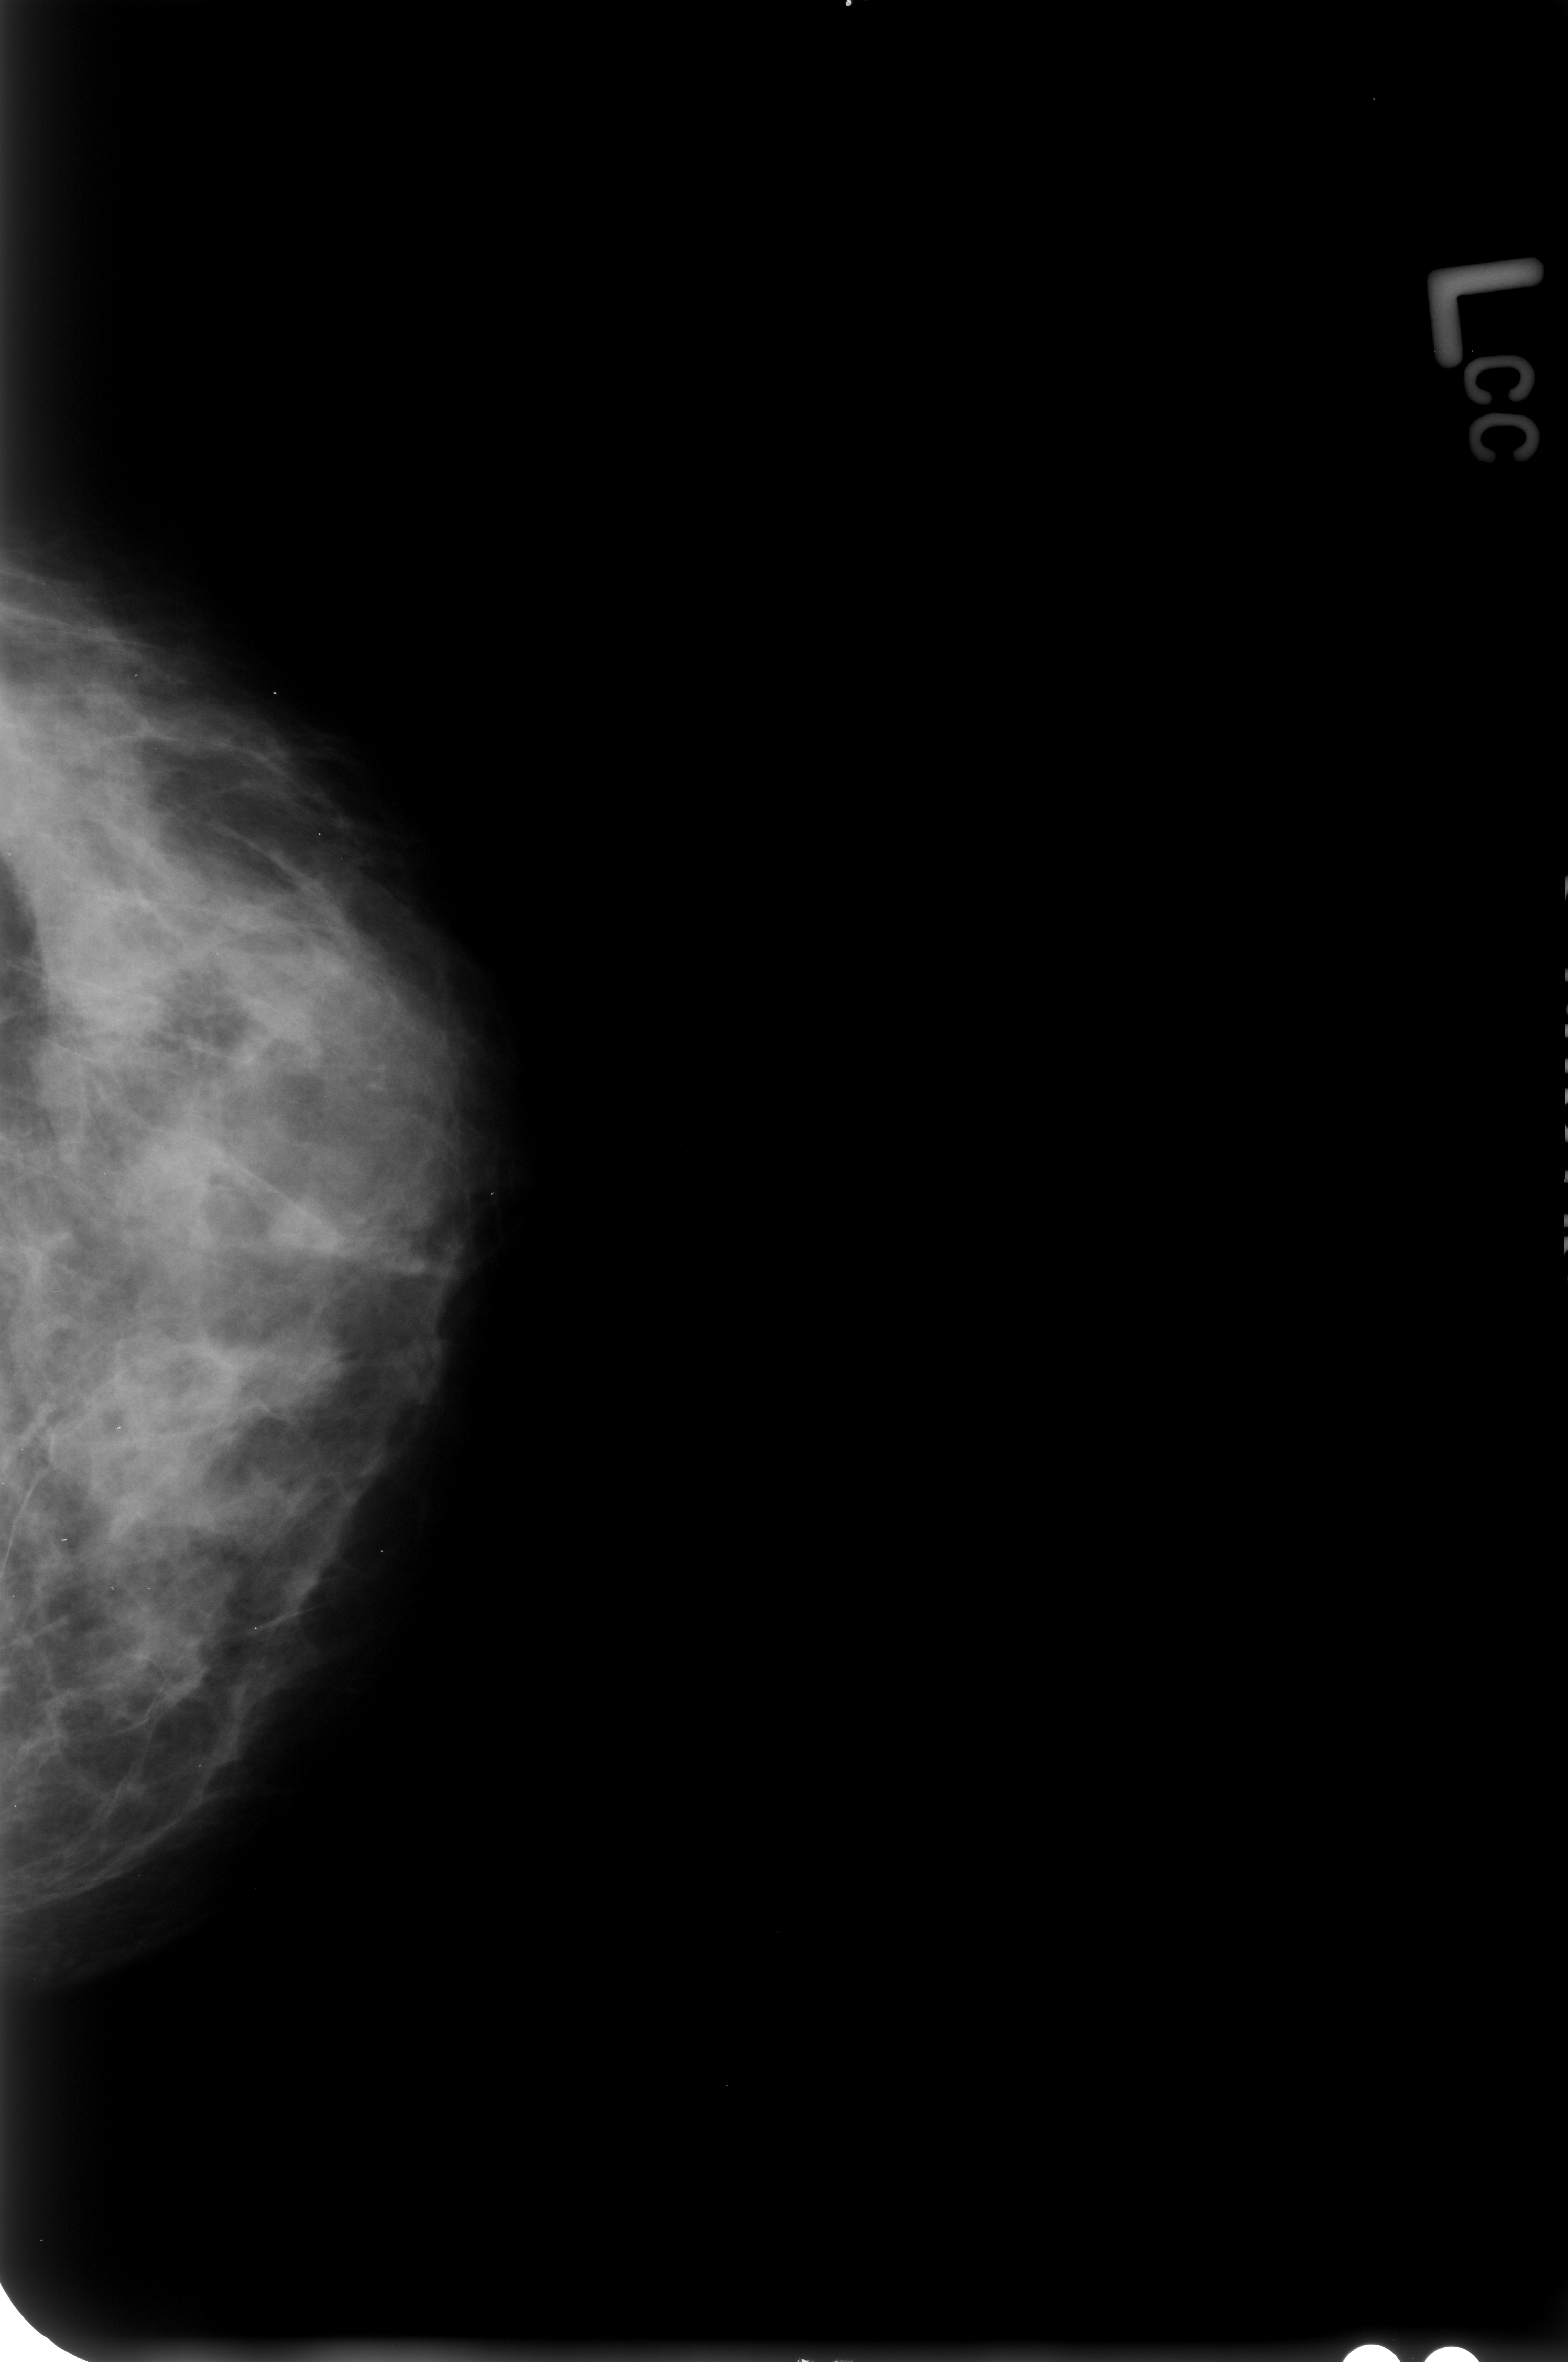
Digitized screen-film mammogram; left breast; craniocaudal (CC) view; BI-RADS breast density category 3 (scale 1–4).
- Finding: calcifications, morphology punctate; BI-RADS assessment category 2; benign without callback (not worked up further).